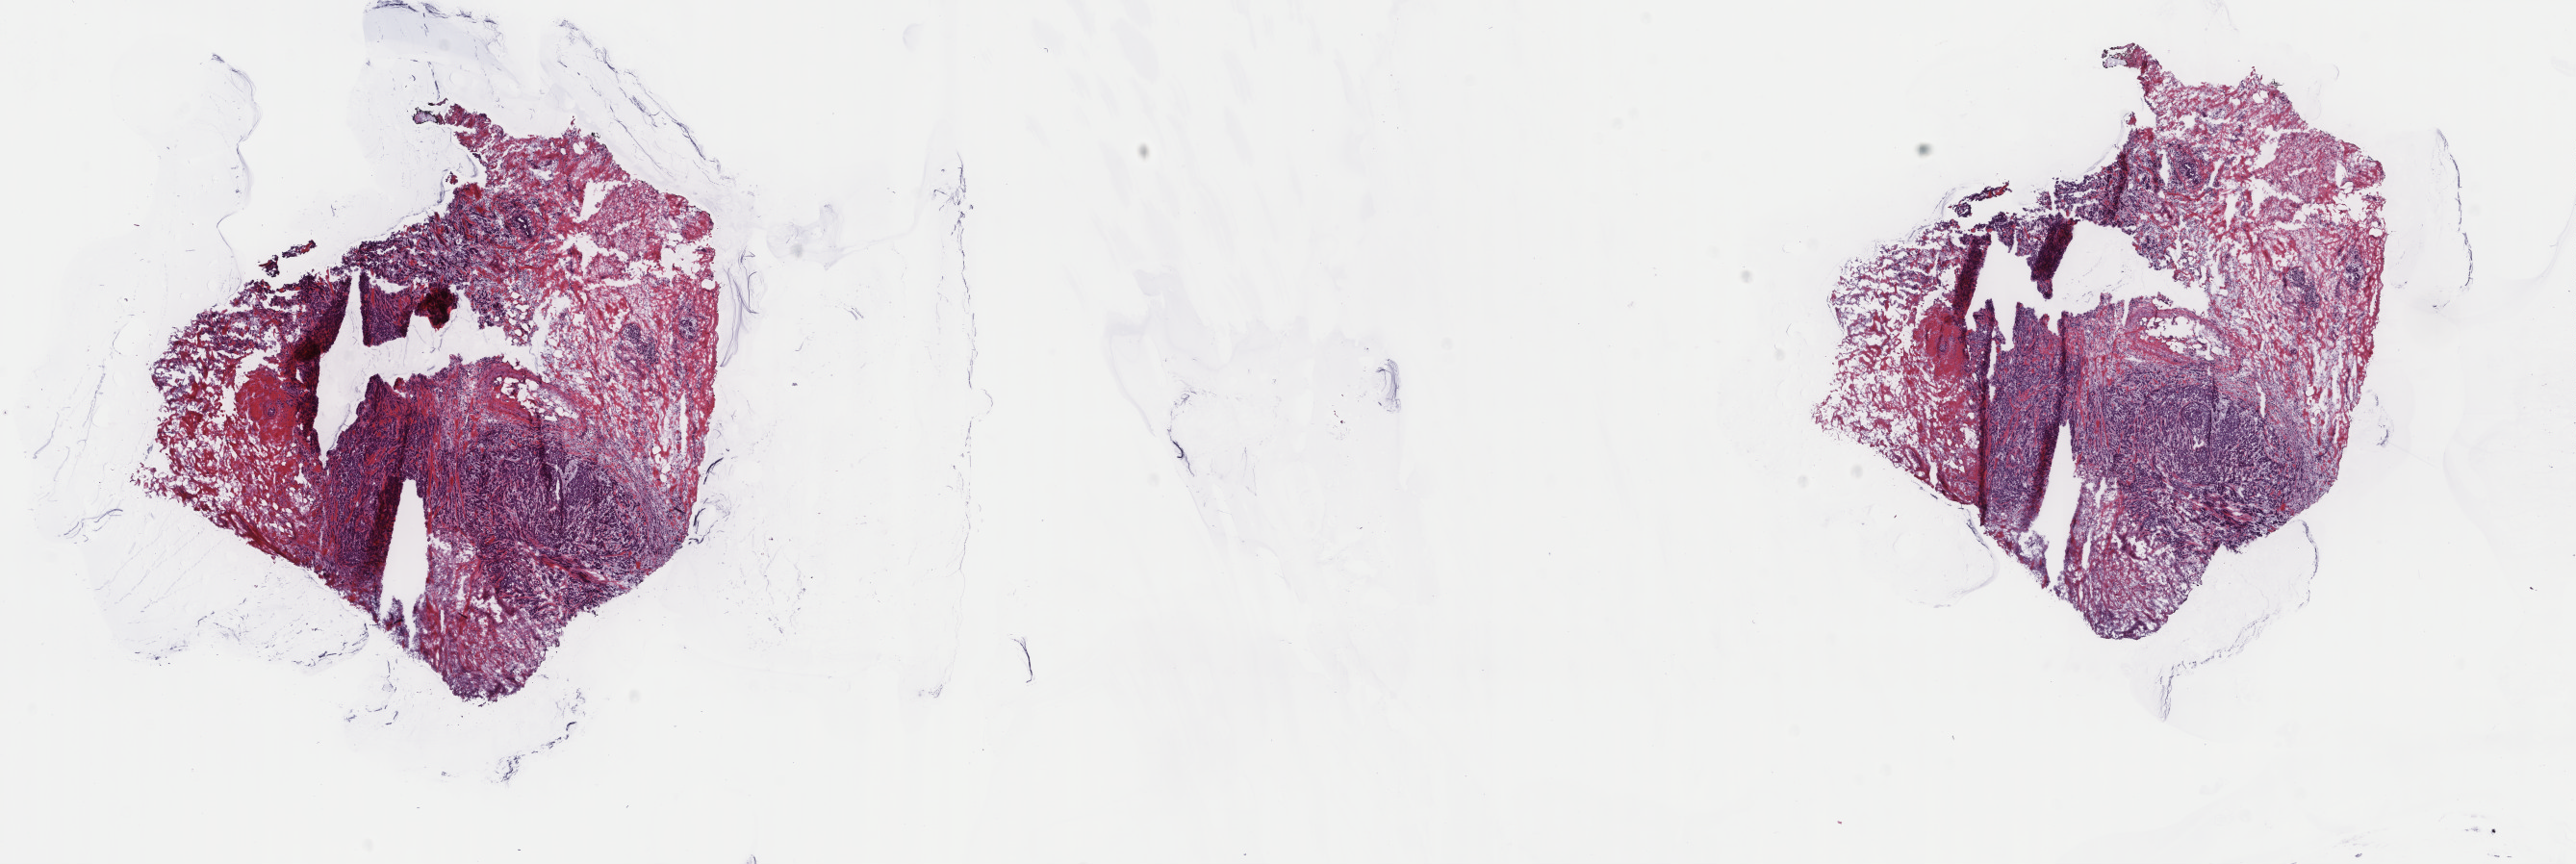
Whole-slide histology image, Hematoxylin and eosin (H&E) stained, shown as a low-resolution overview of the whole scanned area (about 21.2 x 7.1 mm, acquisition: 40x scan). Frozen section from the top of the tissue portion. Sample: primary tumour, breast. Patient: female, age at initial diagnosis 54 years. Composition of this section per pathologist review: tumour cells 25%, tumour nuclei 65%.
Diagnosis: Infiltrating duct carcinoma, NOS.